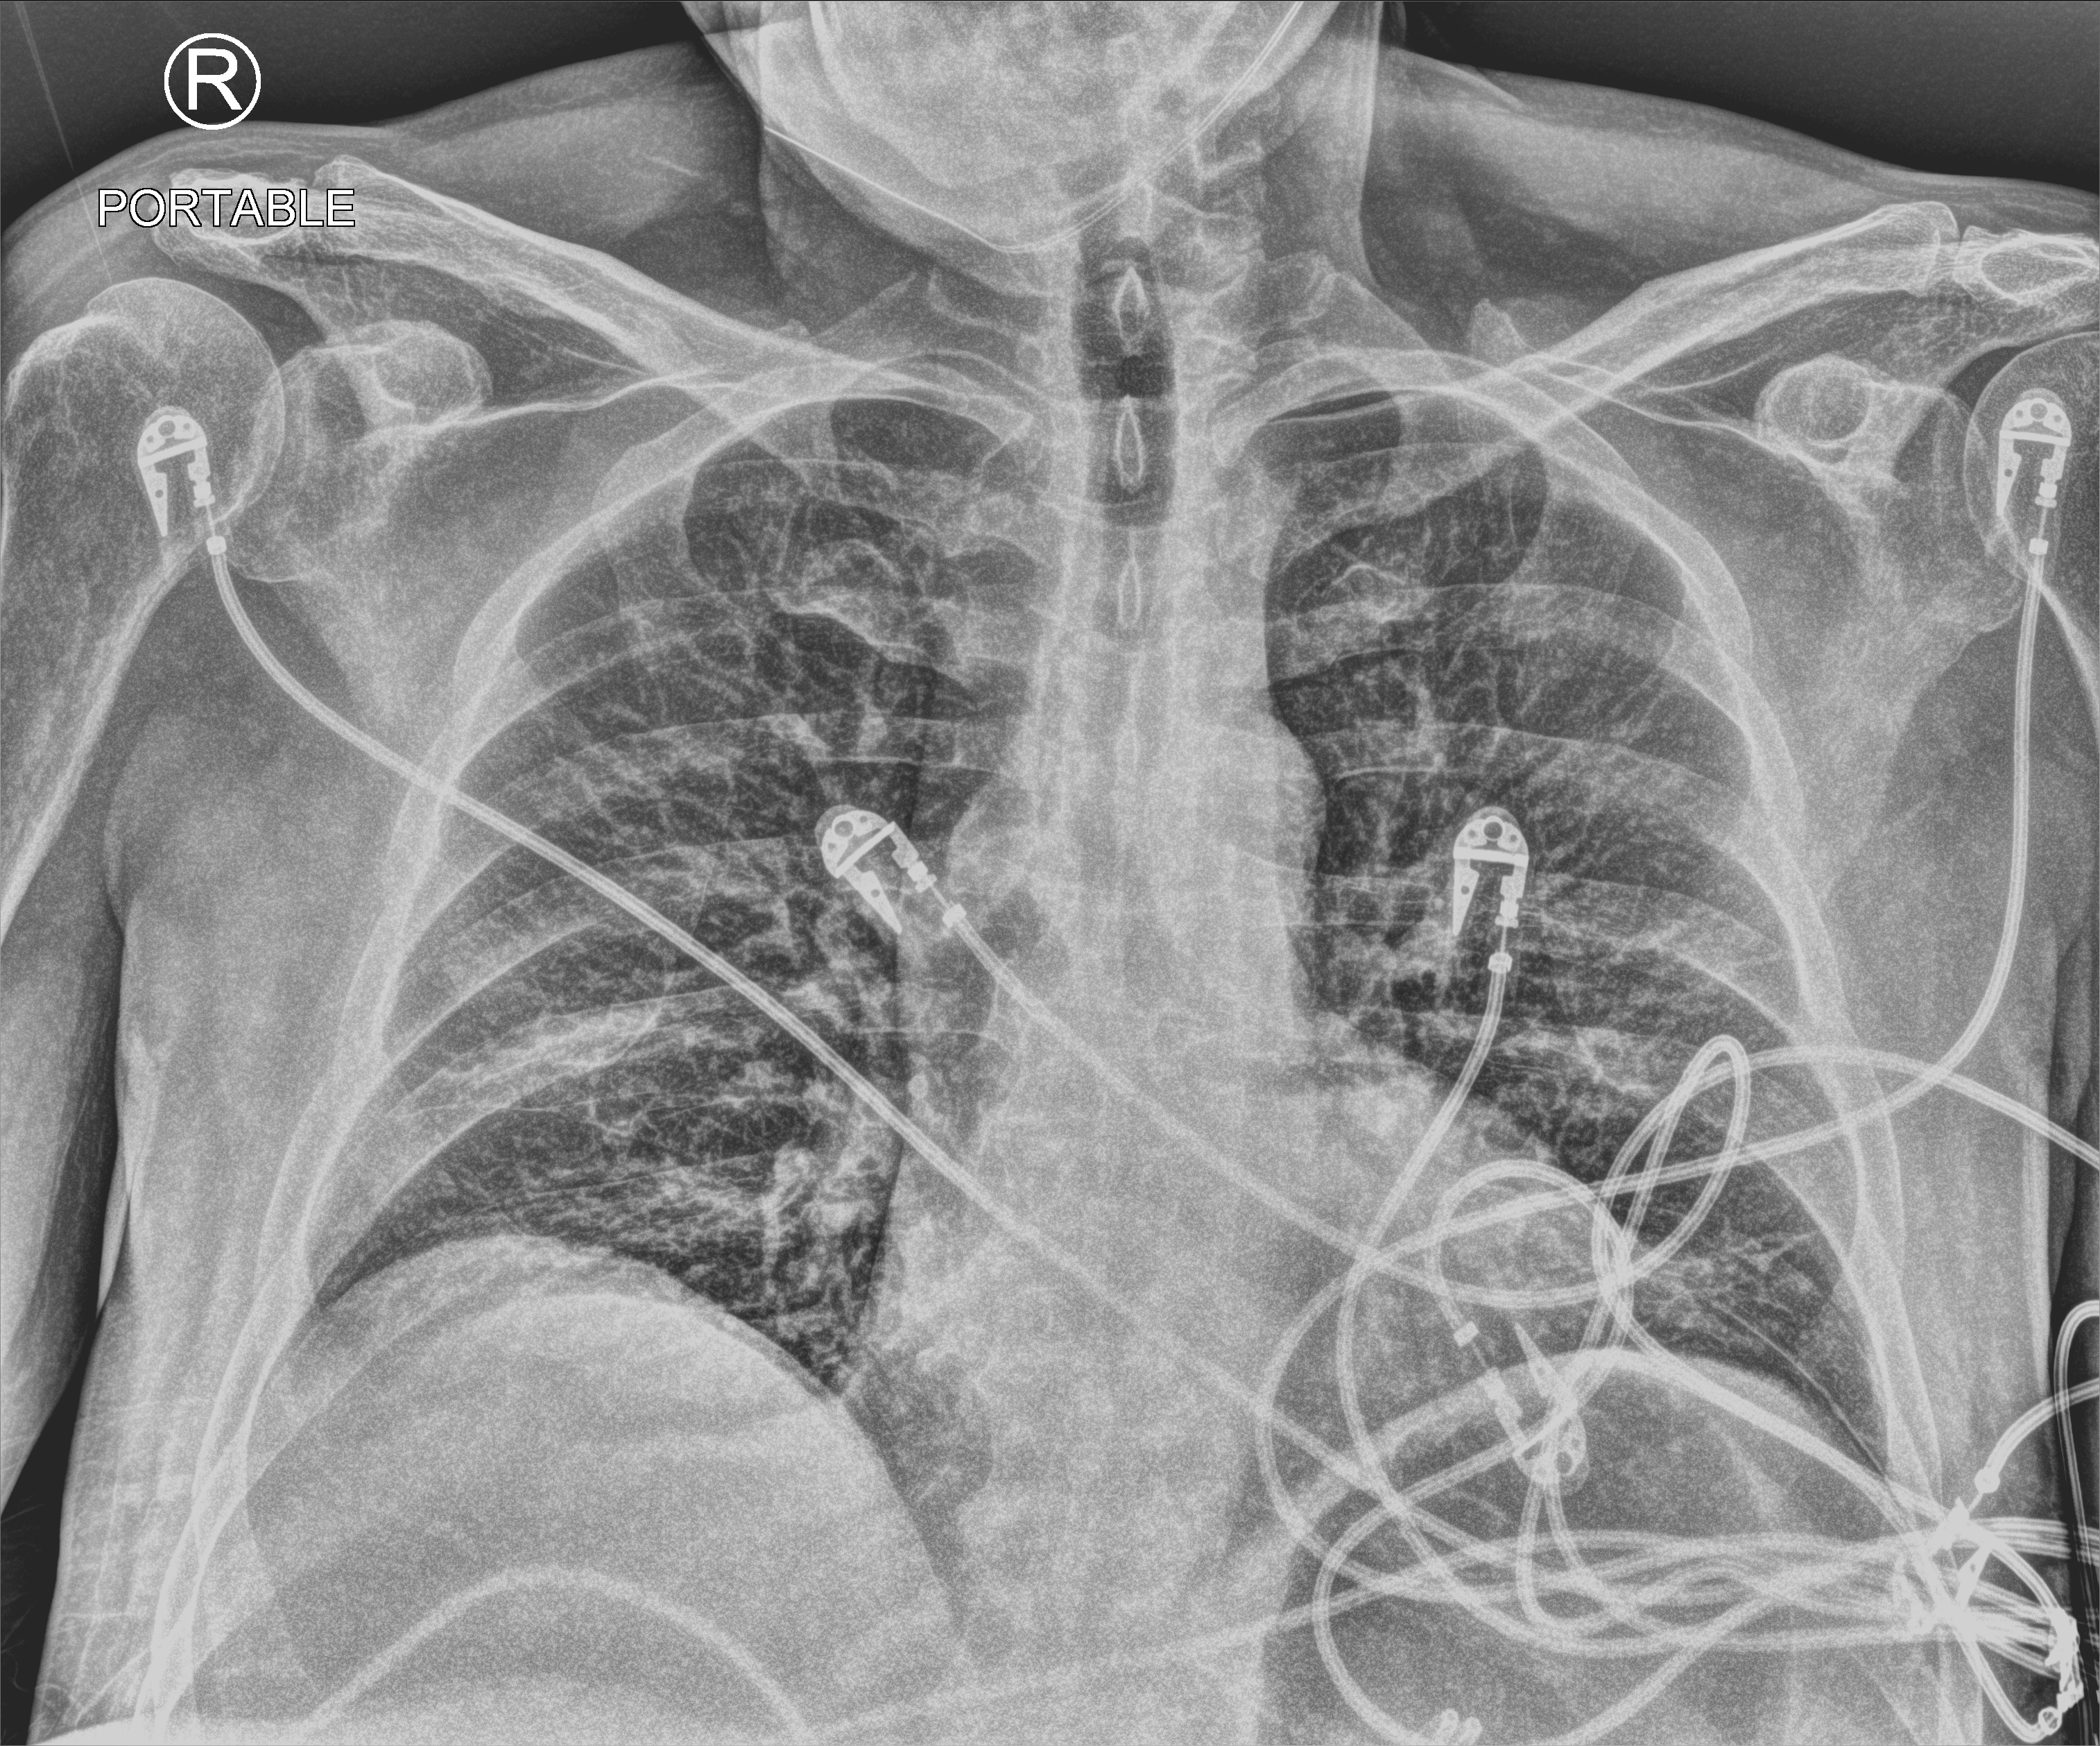
Bedside chest radiograph (computed radiography); anteroposterior (AP) projection. Patient hospitalised with COVID-19; male, aged 60–74 years.
From the hospital-stay record, not from the radiograph (when in the stay this image was taken is not recorded): admitted to intensive care during this hospital stay: yes; mechanically ventilated during this hospital stay: no; COPD (admission record): no.